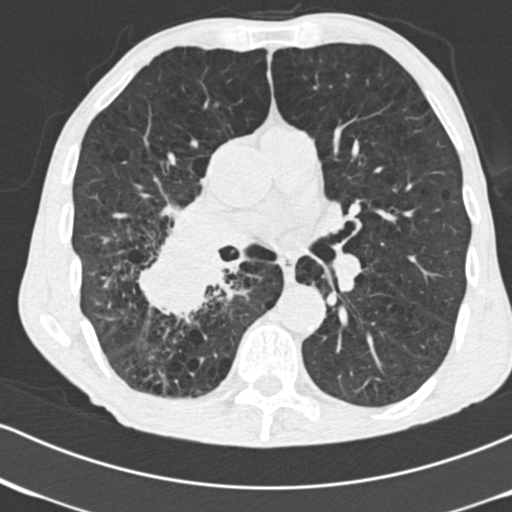
Low-dose screening chest CT, axial slice, second screening round (one year after baseline), lung window (W 1500 / L -600 HU), slice 92 of 182 in the series. Male participant, aged 64 years at enrolment. Current smoker at enrolment.
Lesion marked by an expert reader, bounding box <130,229,239,330> (left, top, right, bottom; pixels). The exam's reader record, not a measurement of the box and not confirmed to be the same lesion: non-calcified nodule or mass ≥4 mm, 52 × 37 mm, spiculated (stellate) margins, soft tissue attenuation, pre-existing on the prior screen: no.